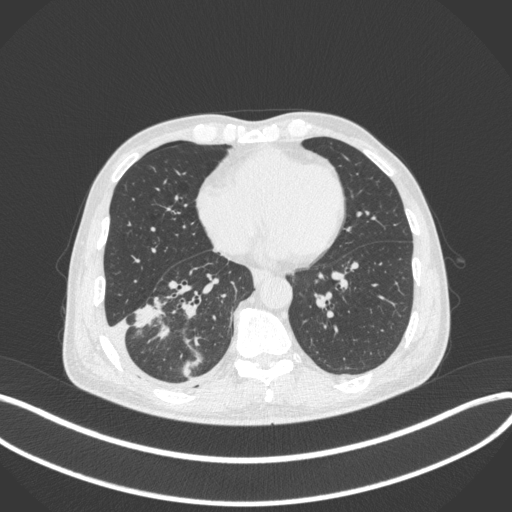
Chest CT, one axial slice. Slice 144 of 385 in the series (ordered by position). Reconstruction kernel B31f. 120 kVp. Lung window (W 1500 / L -600 HU). 512 × 512 image matrix, field of view 400 × 400 mm. Male patient, age 64 years. Case-level facts recorded for this patient, not image findings: clinical TNM (as recorded): T3 N0 M0.
Annotated regions visible in this slice (bounding box drawn by a radiologist):
- lung tumour (recorded histology: adenocarcinoma): box from (x=131, y=296) to (x=170, y=342) px